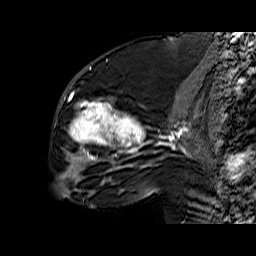
Breast MRI (dynamic contrast-enhanced), one sagittal slice; slice 29 of 60 in the series (ordered by position); dynamic contrast-enhanced series, time point 2 of 6 at this slice position (early post-contrast); 1.5 T; TE 6.4 ms, TR 32.9 ms; 4 mm slice thickness; 256 × 256 image matrix, field of view 200 × 200 mm. Female patient. From the clinical record (not read from this slice): setting: breast cancer imaged before/during neoadjuvant chemotherapy; receptor status: triple-negative.
Structures marked on this image (semi-automatic segmentation, software-assisted and operator-edited):
- analysis volume of interest (the breast-tissue region the enhancement analysis was run in; not a lesion): bounding box (x1, y1, x2, y2) in pixels: (56, 65, 159, 174)
- tumour enhancement mask (voxels above the 100 % enhancement threshold inside the analysis volume of interest): (69, 96, 158, 169)